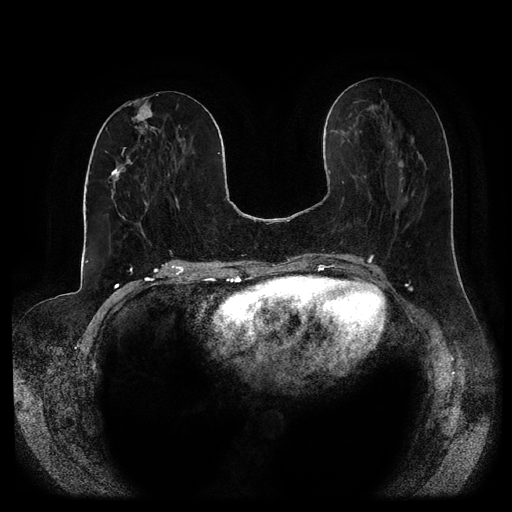
Breast MRI (dynamic contrast-enhanced, multi-phase), one axial slice. Slice 42 of 116 in the series (ordered by position). Dynamic contrast-enhanced series, time point 2 of 5 at this slice position (early post-contrast). 1.5 T. TE 2.6 ms, TR 5.2 ms. 2 mm slice thickness. 512 × 512 image matrix. Patient: female, 53 years.
Outlined on this slice (semi-automatically segmented with operator editing):
- breast lesion (labelled 'tumour' in the annotation; benign lesions carry a separate 'benign' label): bounding box <131,97,154,131> (left, top, right, bottom; pixels)
- breast lesion (labelled 'tumour' in the annotation; benign lesions carry a separate 'benign' label): <111,147,133,184>